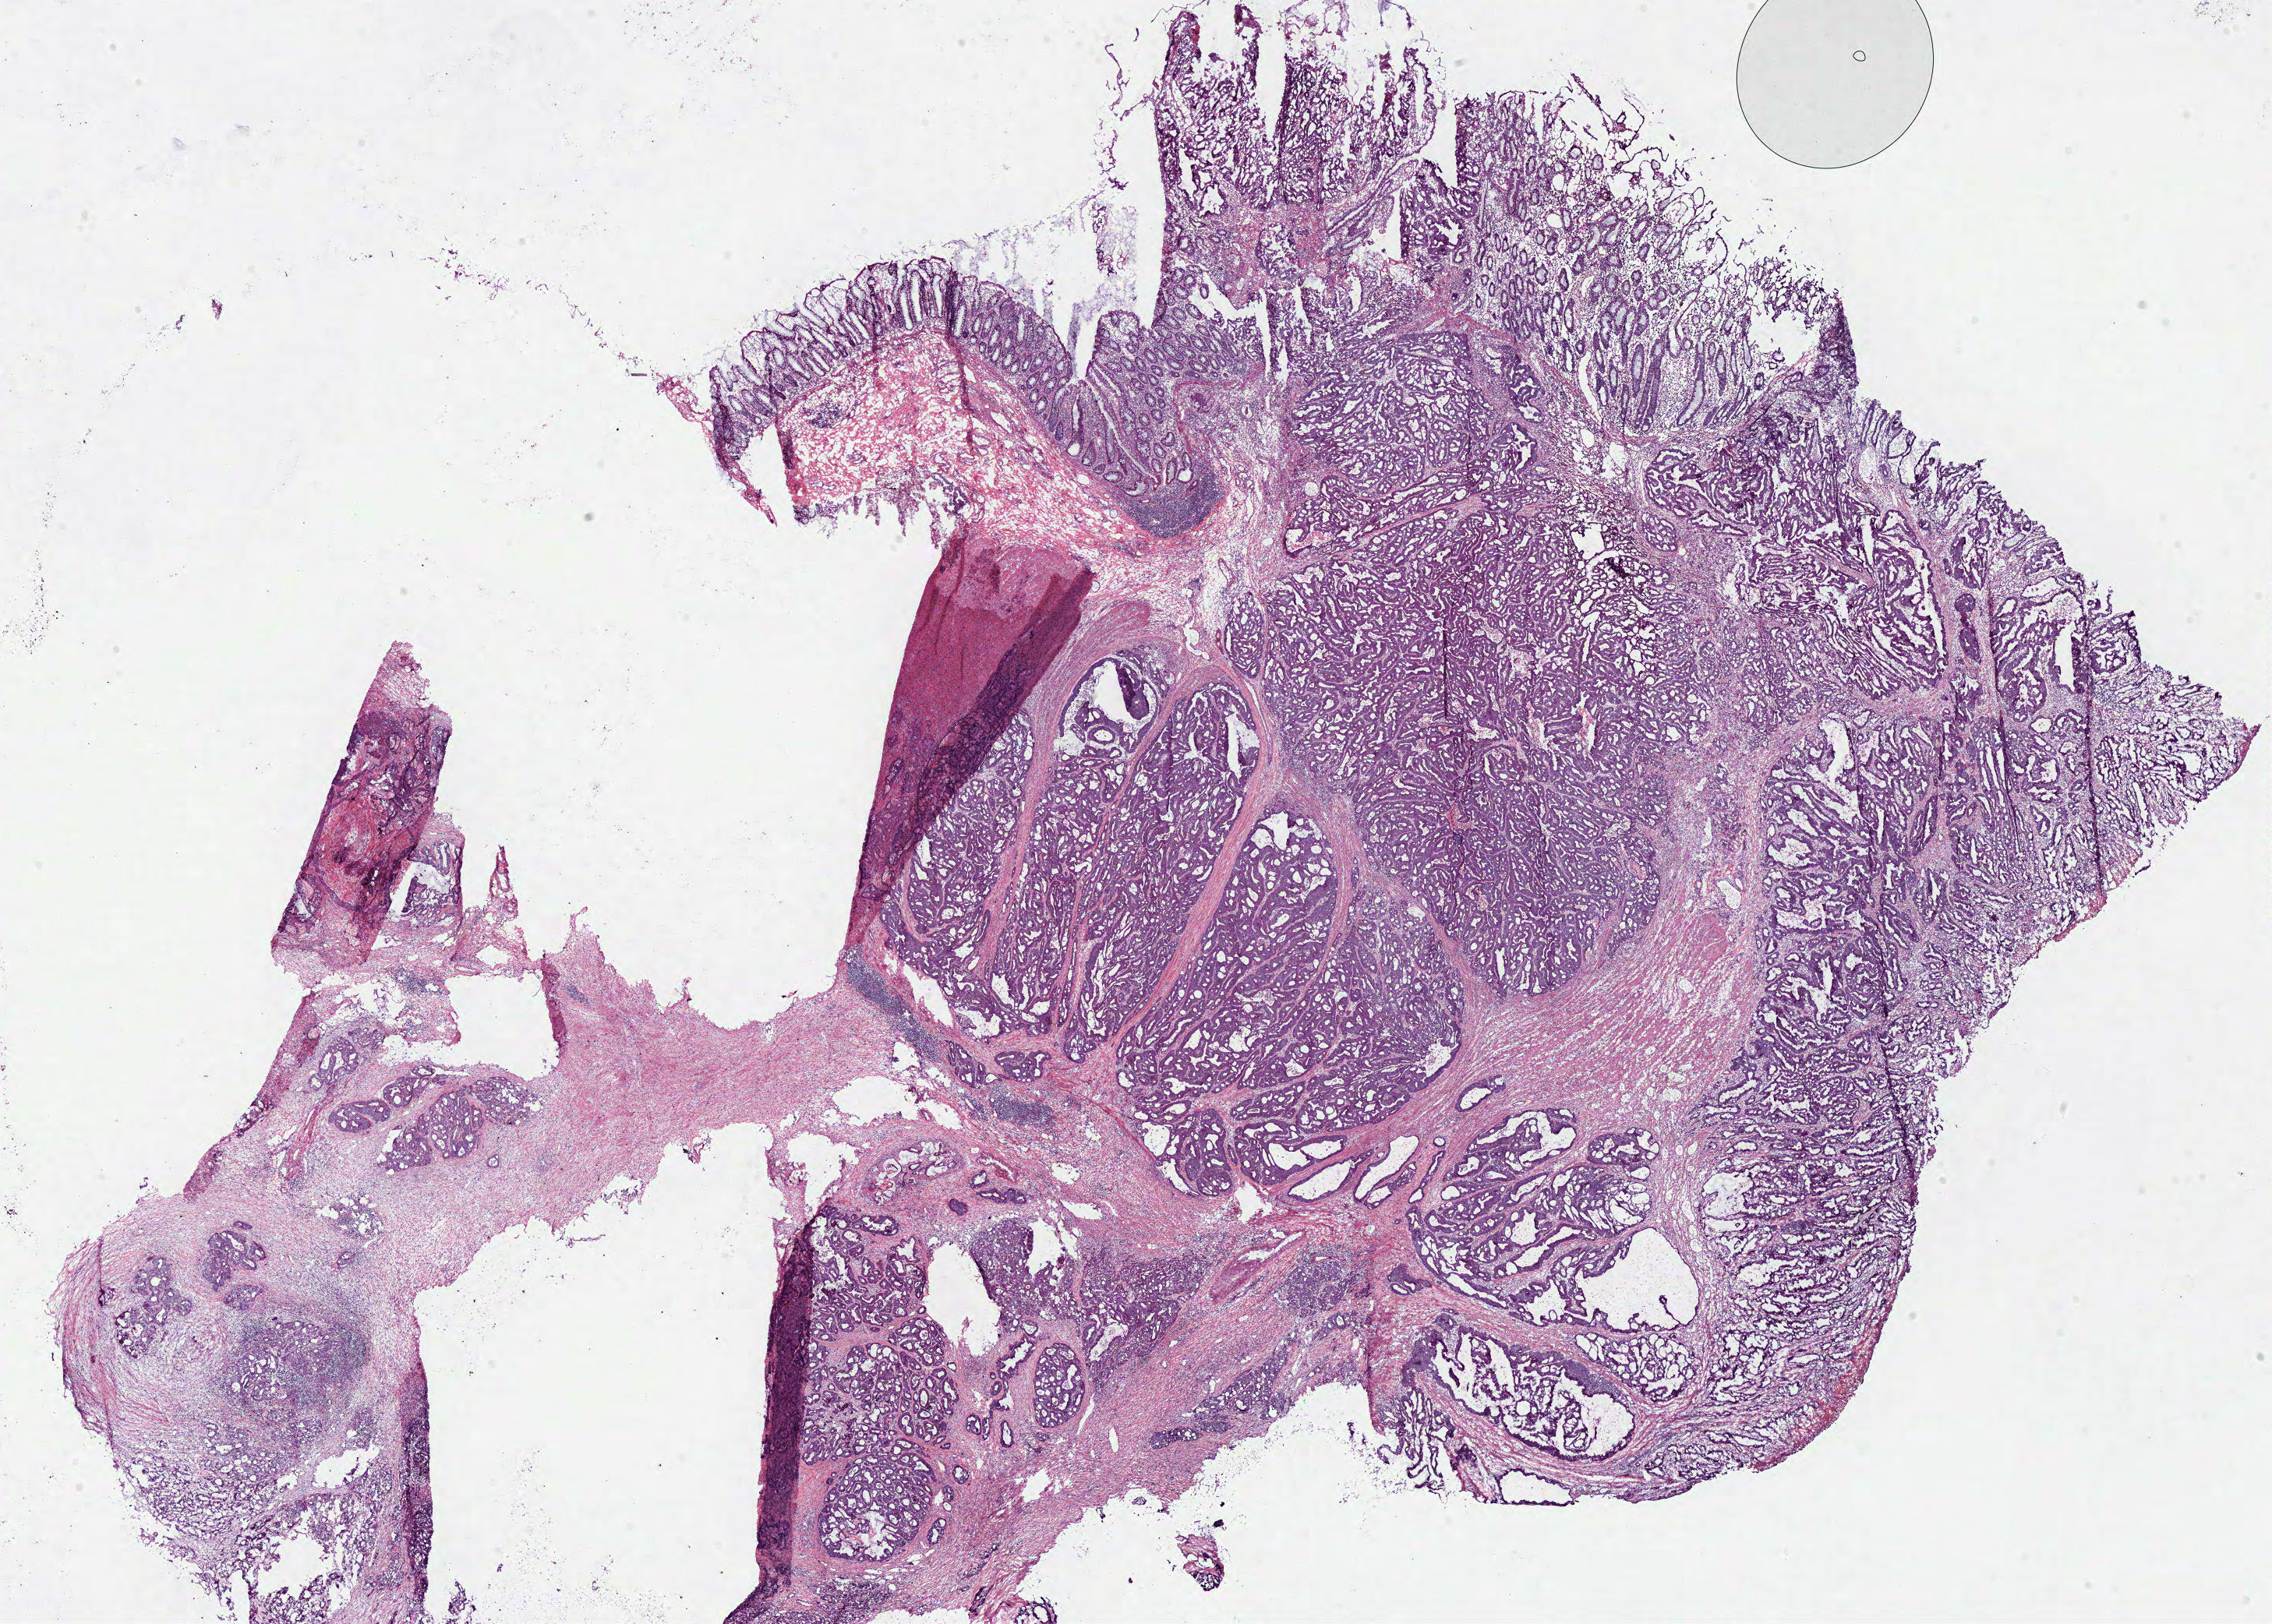
Whole-slide histology image, Hematoxylin and eosin (H&E) stained, low-resolution overview of the scanned area, about 23.0 x 16.4 mm (from a 40x scan); frozen section; primary tumour sample from the colon. Female patient; age at initial diagnosis 52 years. Composition of this section per pathologist review: tumour cells 72%, tumour nuclei 80%, normal cells 8%, stromal cells 15%, necrosis 5%.
TNM: T3 N1 M1. AJCC pathologic stage: IVA (7th edition). Histologic diagnosis: Adenocarcinoma, NOS (sigmoid colon).